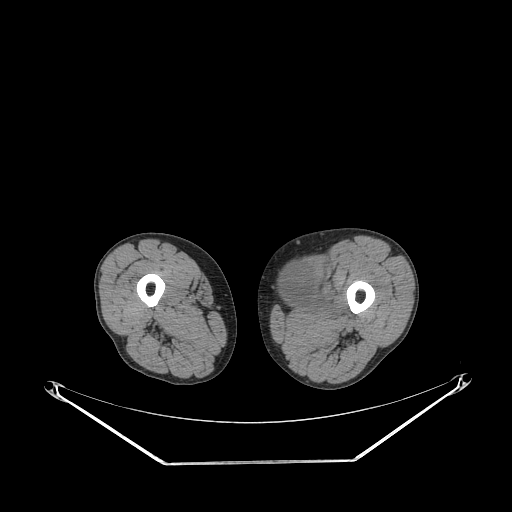
CT of an extremity soft-tissue mass (from a PET/CT study), one axial slice. Position 227 of 267 along the scan axis. Reconstruction kernel STANDARD. Soft-tissue window (W 400 / L 40 HU). 3.75 mm slice thickness. 512 × 512 image matrix, field of view 500 × 500 mm. Male patient. From the clinical record (not read from this slice): histological type: pleiomorphic liposarcoma; grade: high; site of the primary tumour: left thigh.
Outlined on this slice (expert contour drawn on MRI and transferred to this co-registered scan by the dataset authors):
- gross tumour volume including surrounding oedema: box from (x=281, y=262) to (x=343, y=316) px
- gross tumour volume (mass): (x=281, y=262)–(x=316, y=305)